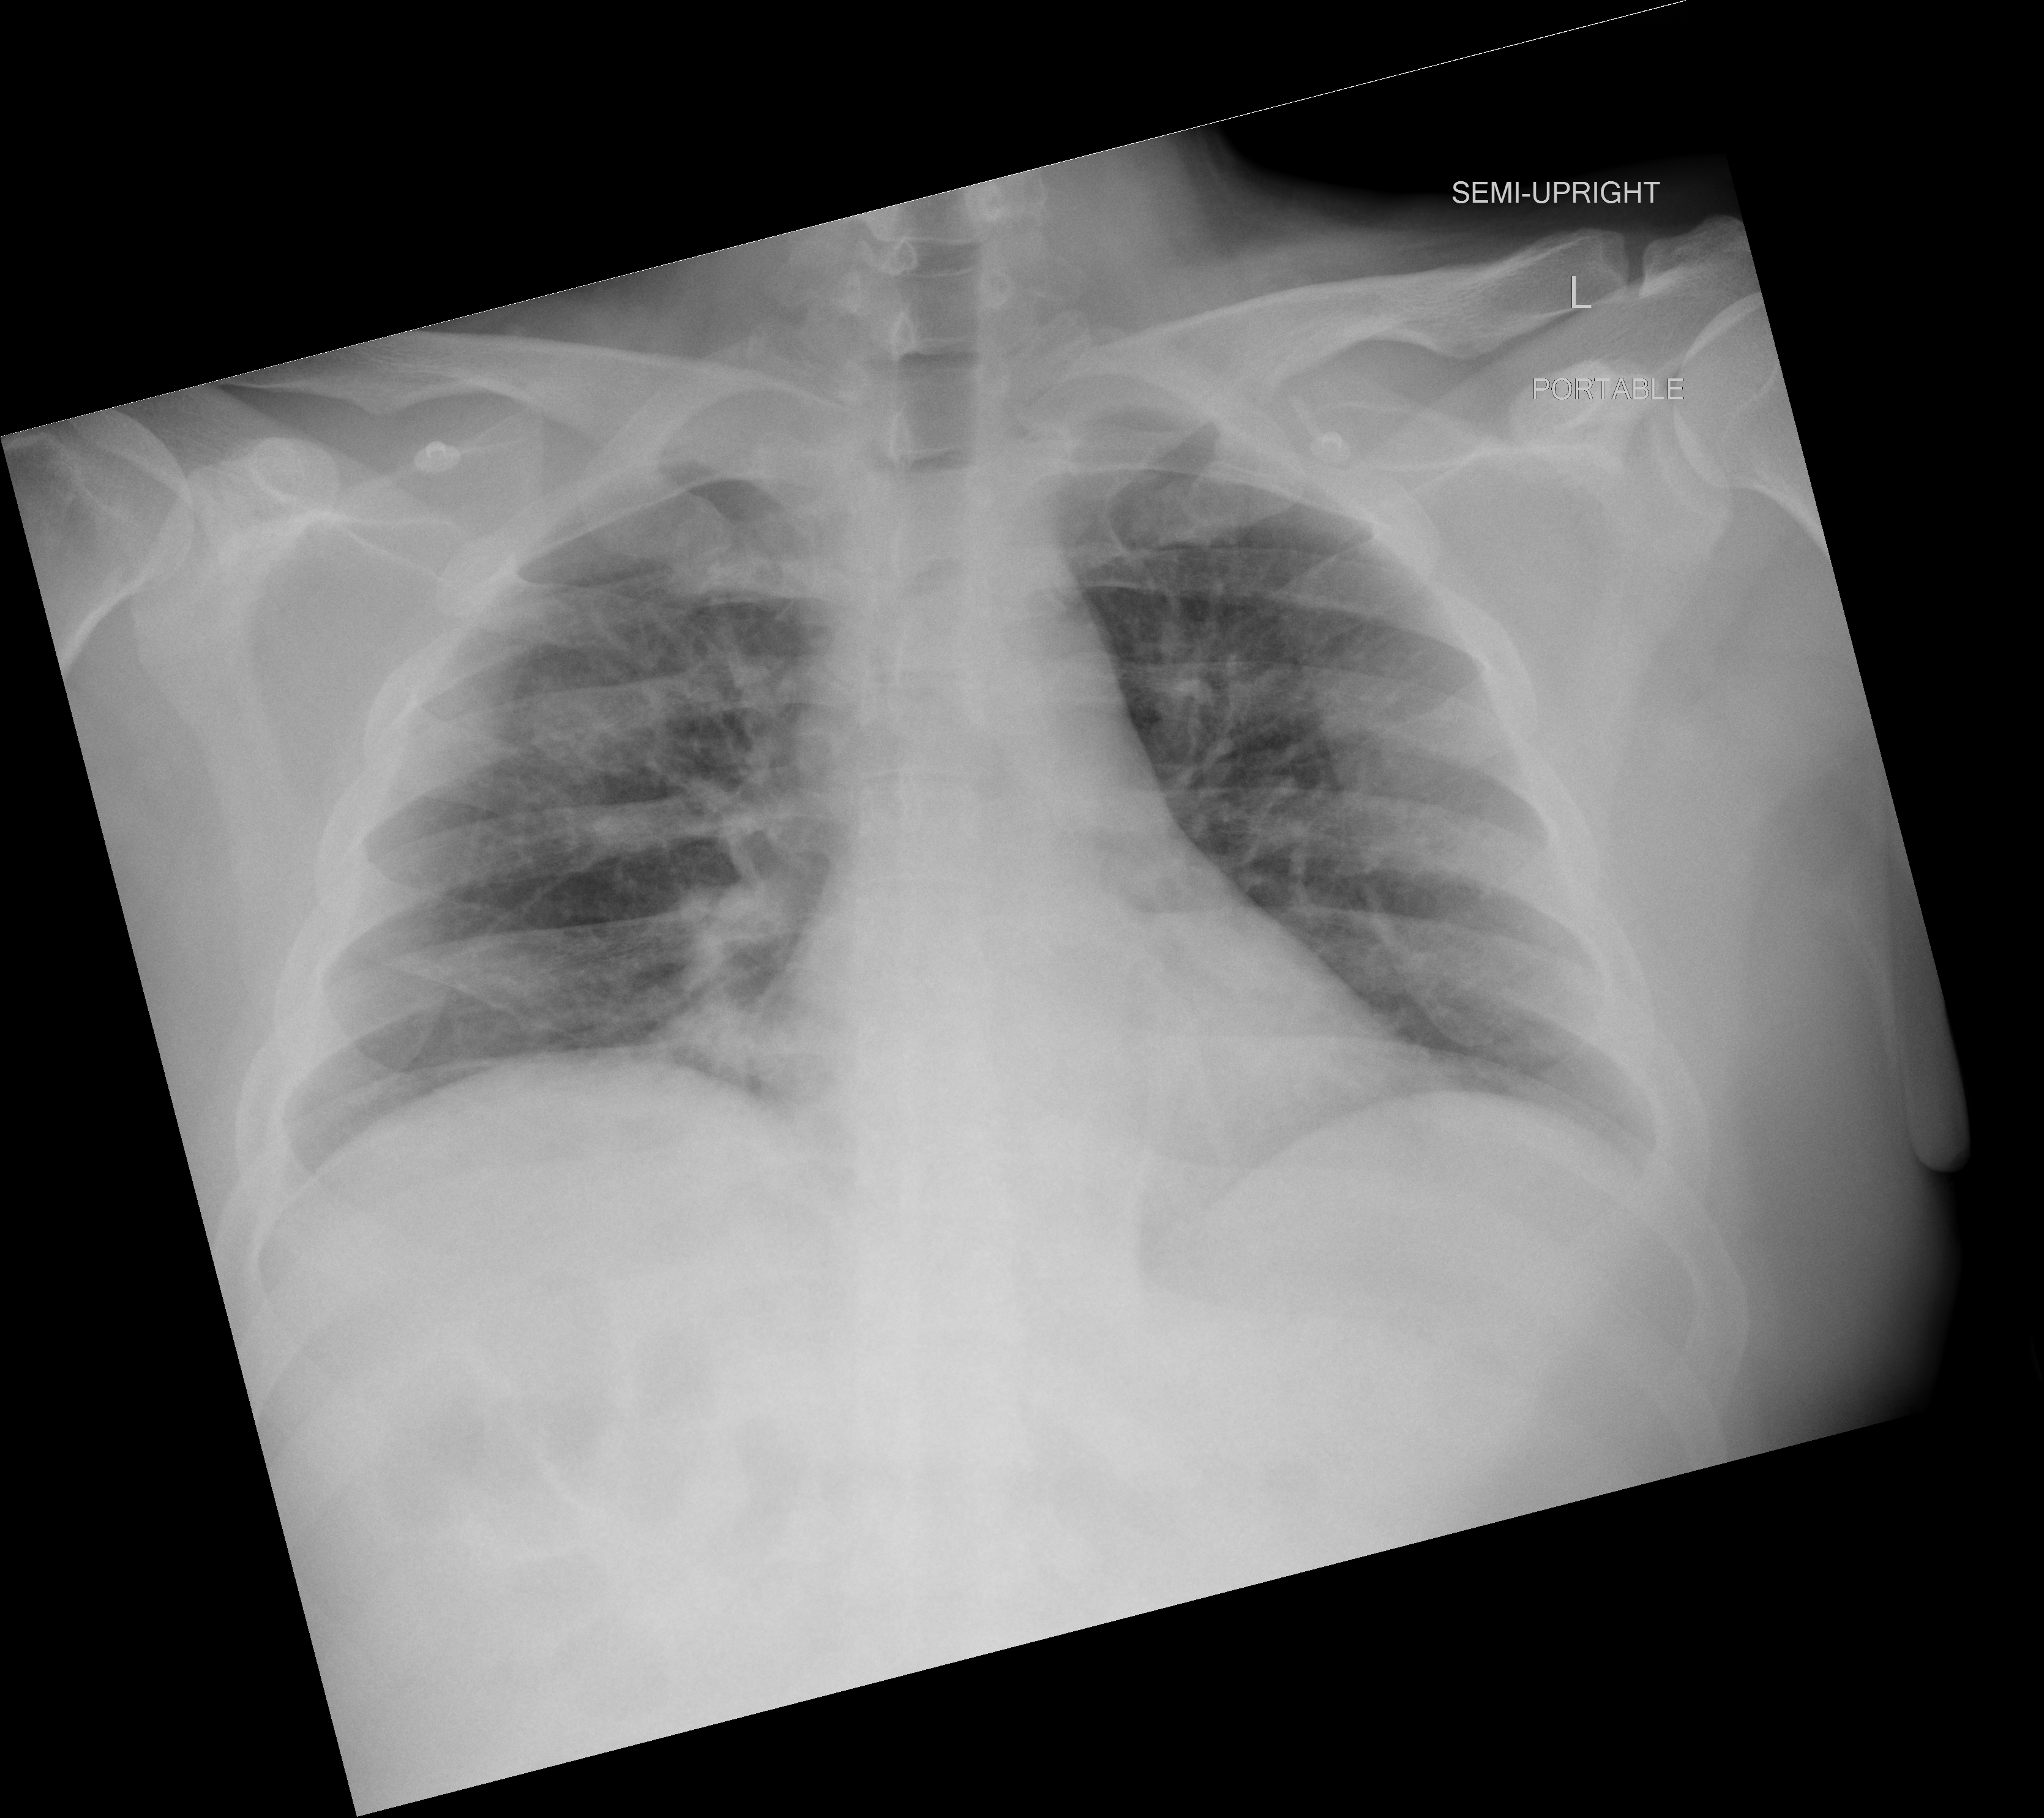
Chest X-ray, AP projection. Male patient, age 38 years; COVID-19 (test-positive).
Radiologist's key findings for this exam: Minimal interval improvement in patchy bilateral airspace opacities.